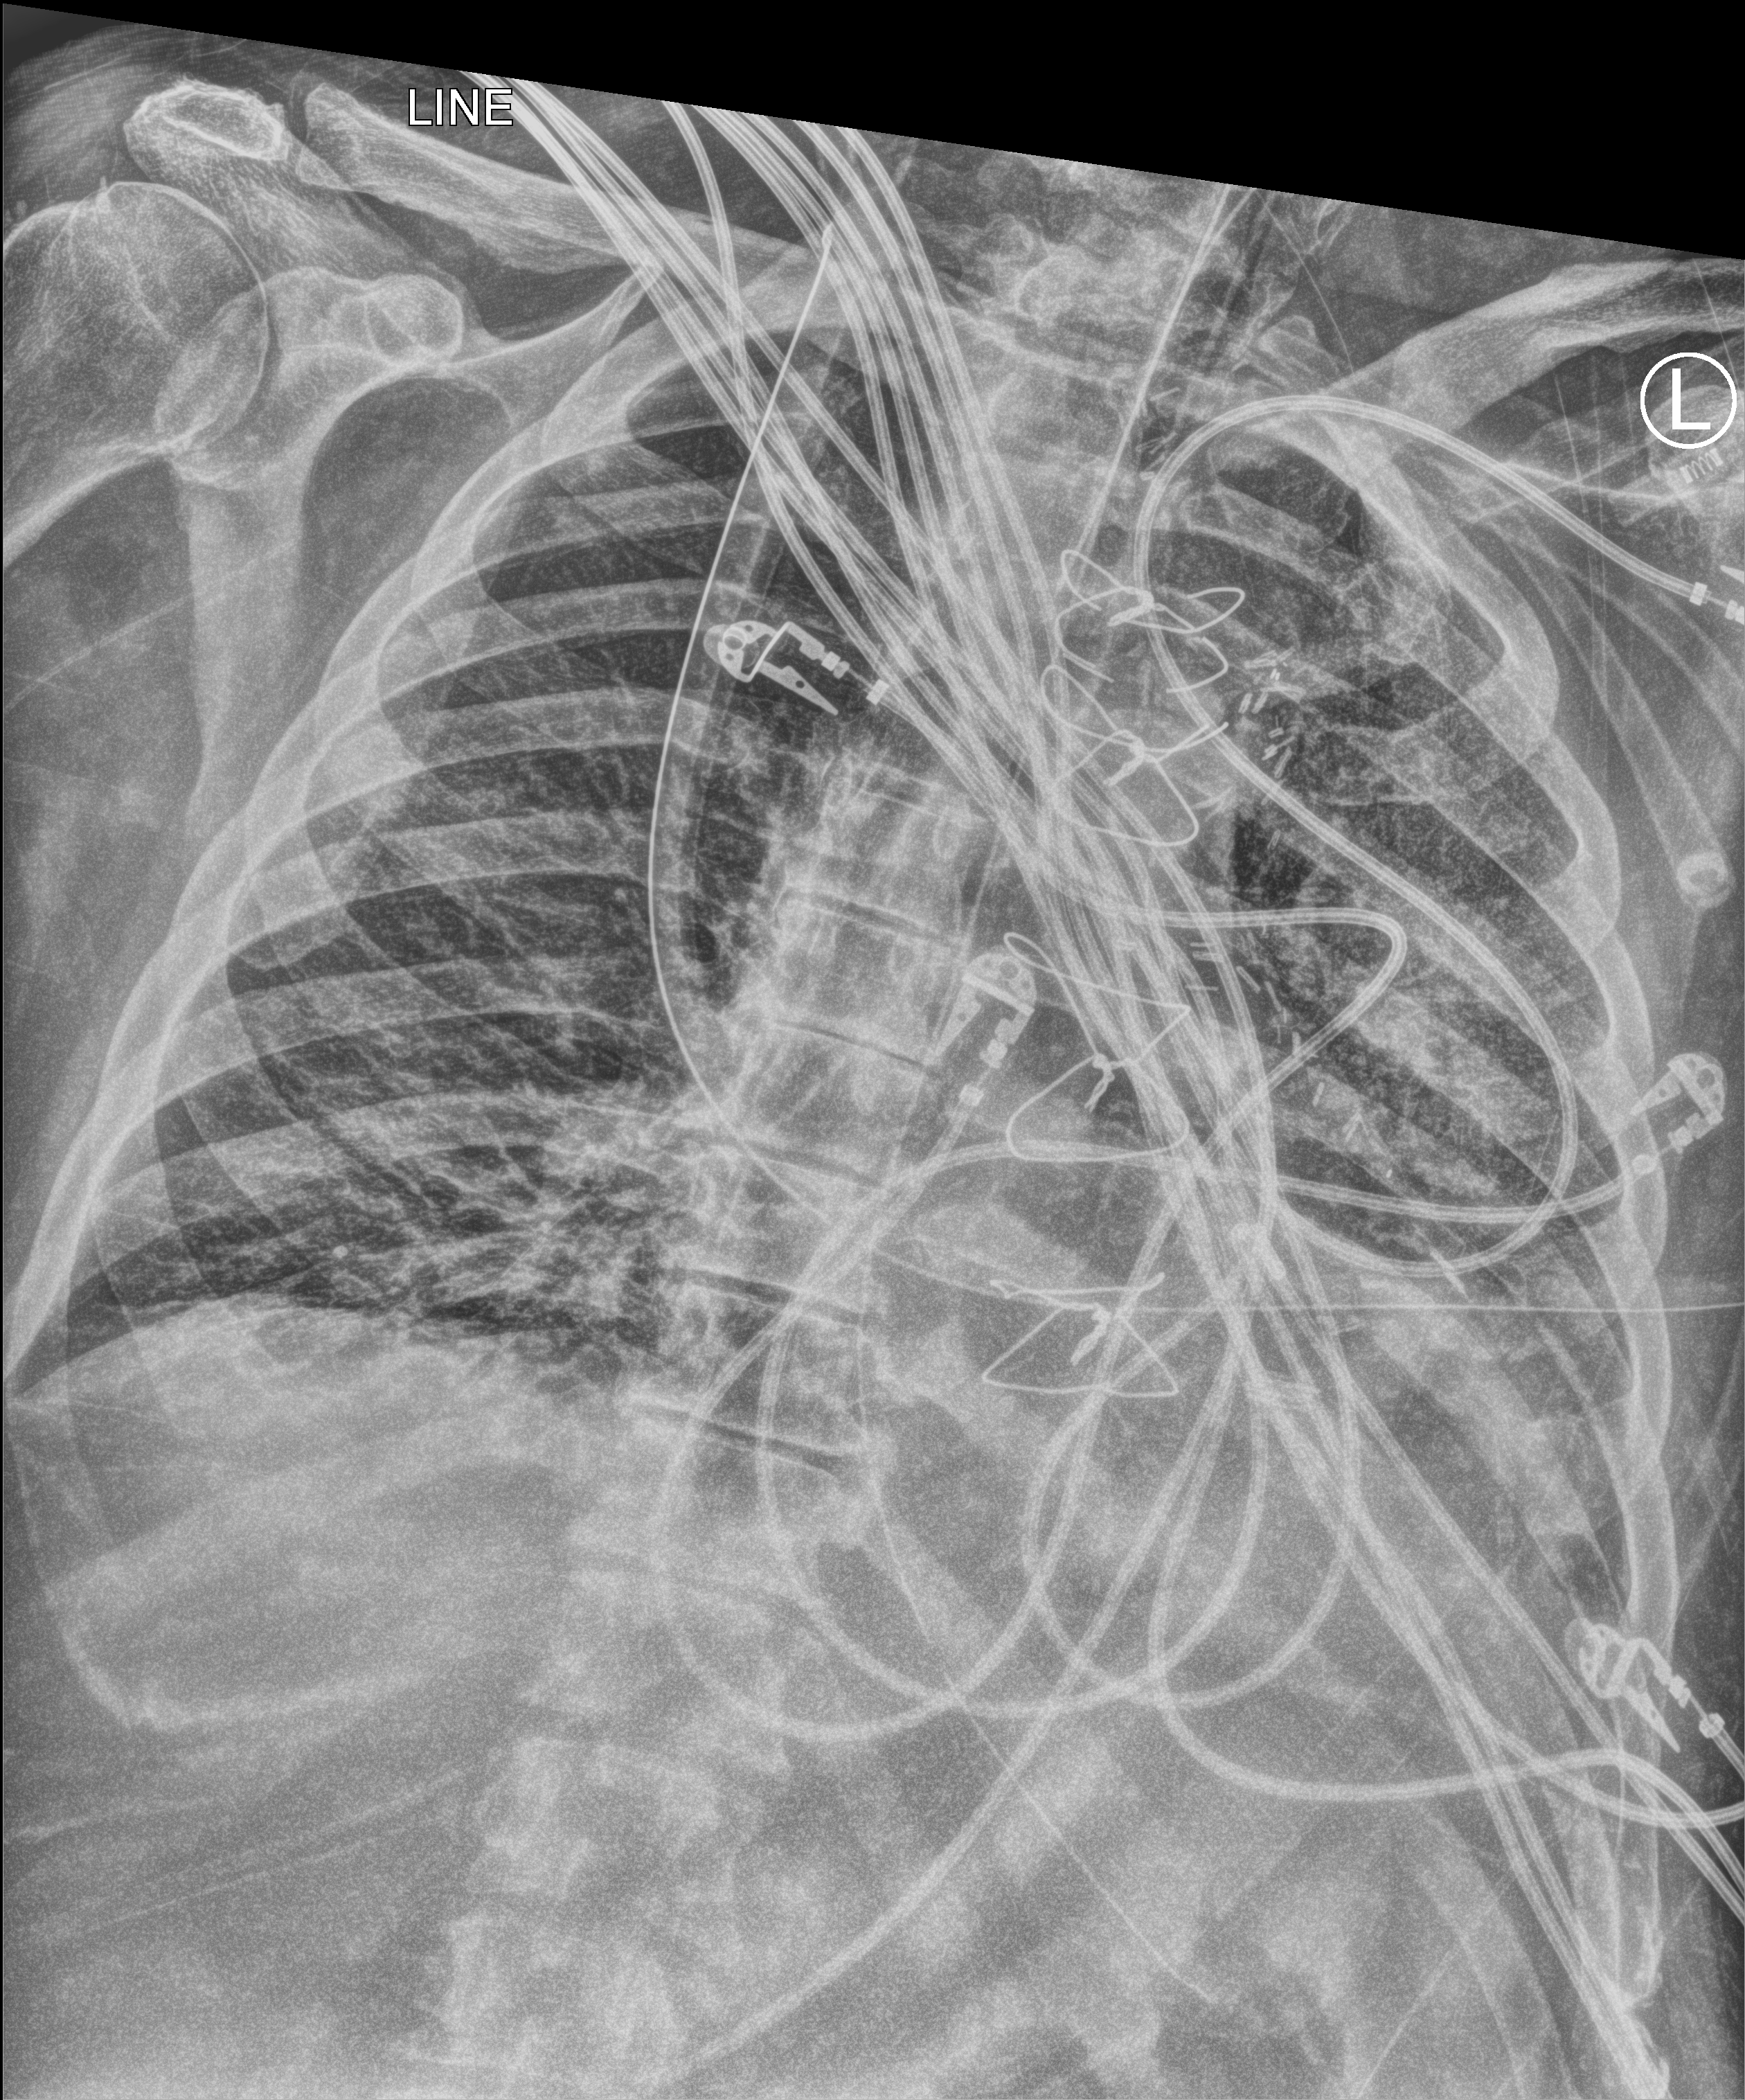
Bedside chest radiograph (computed radiography). Patient hospitalised with COVID-19; male, aged 60–74 years.
From the hospital-stay record, not from the radiograph (when in the stay this image was taken is not recorded): length of hospital stay: 16 days; hypertension (admission record): yes.